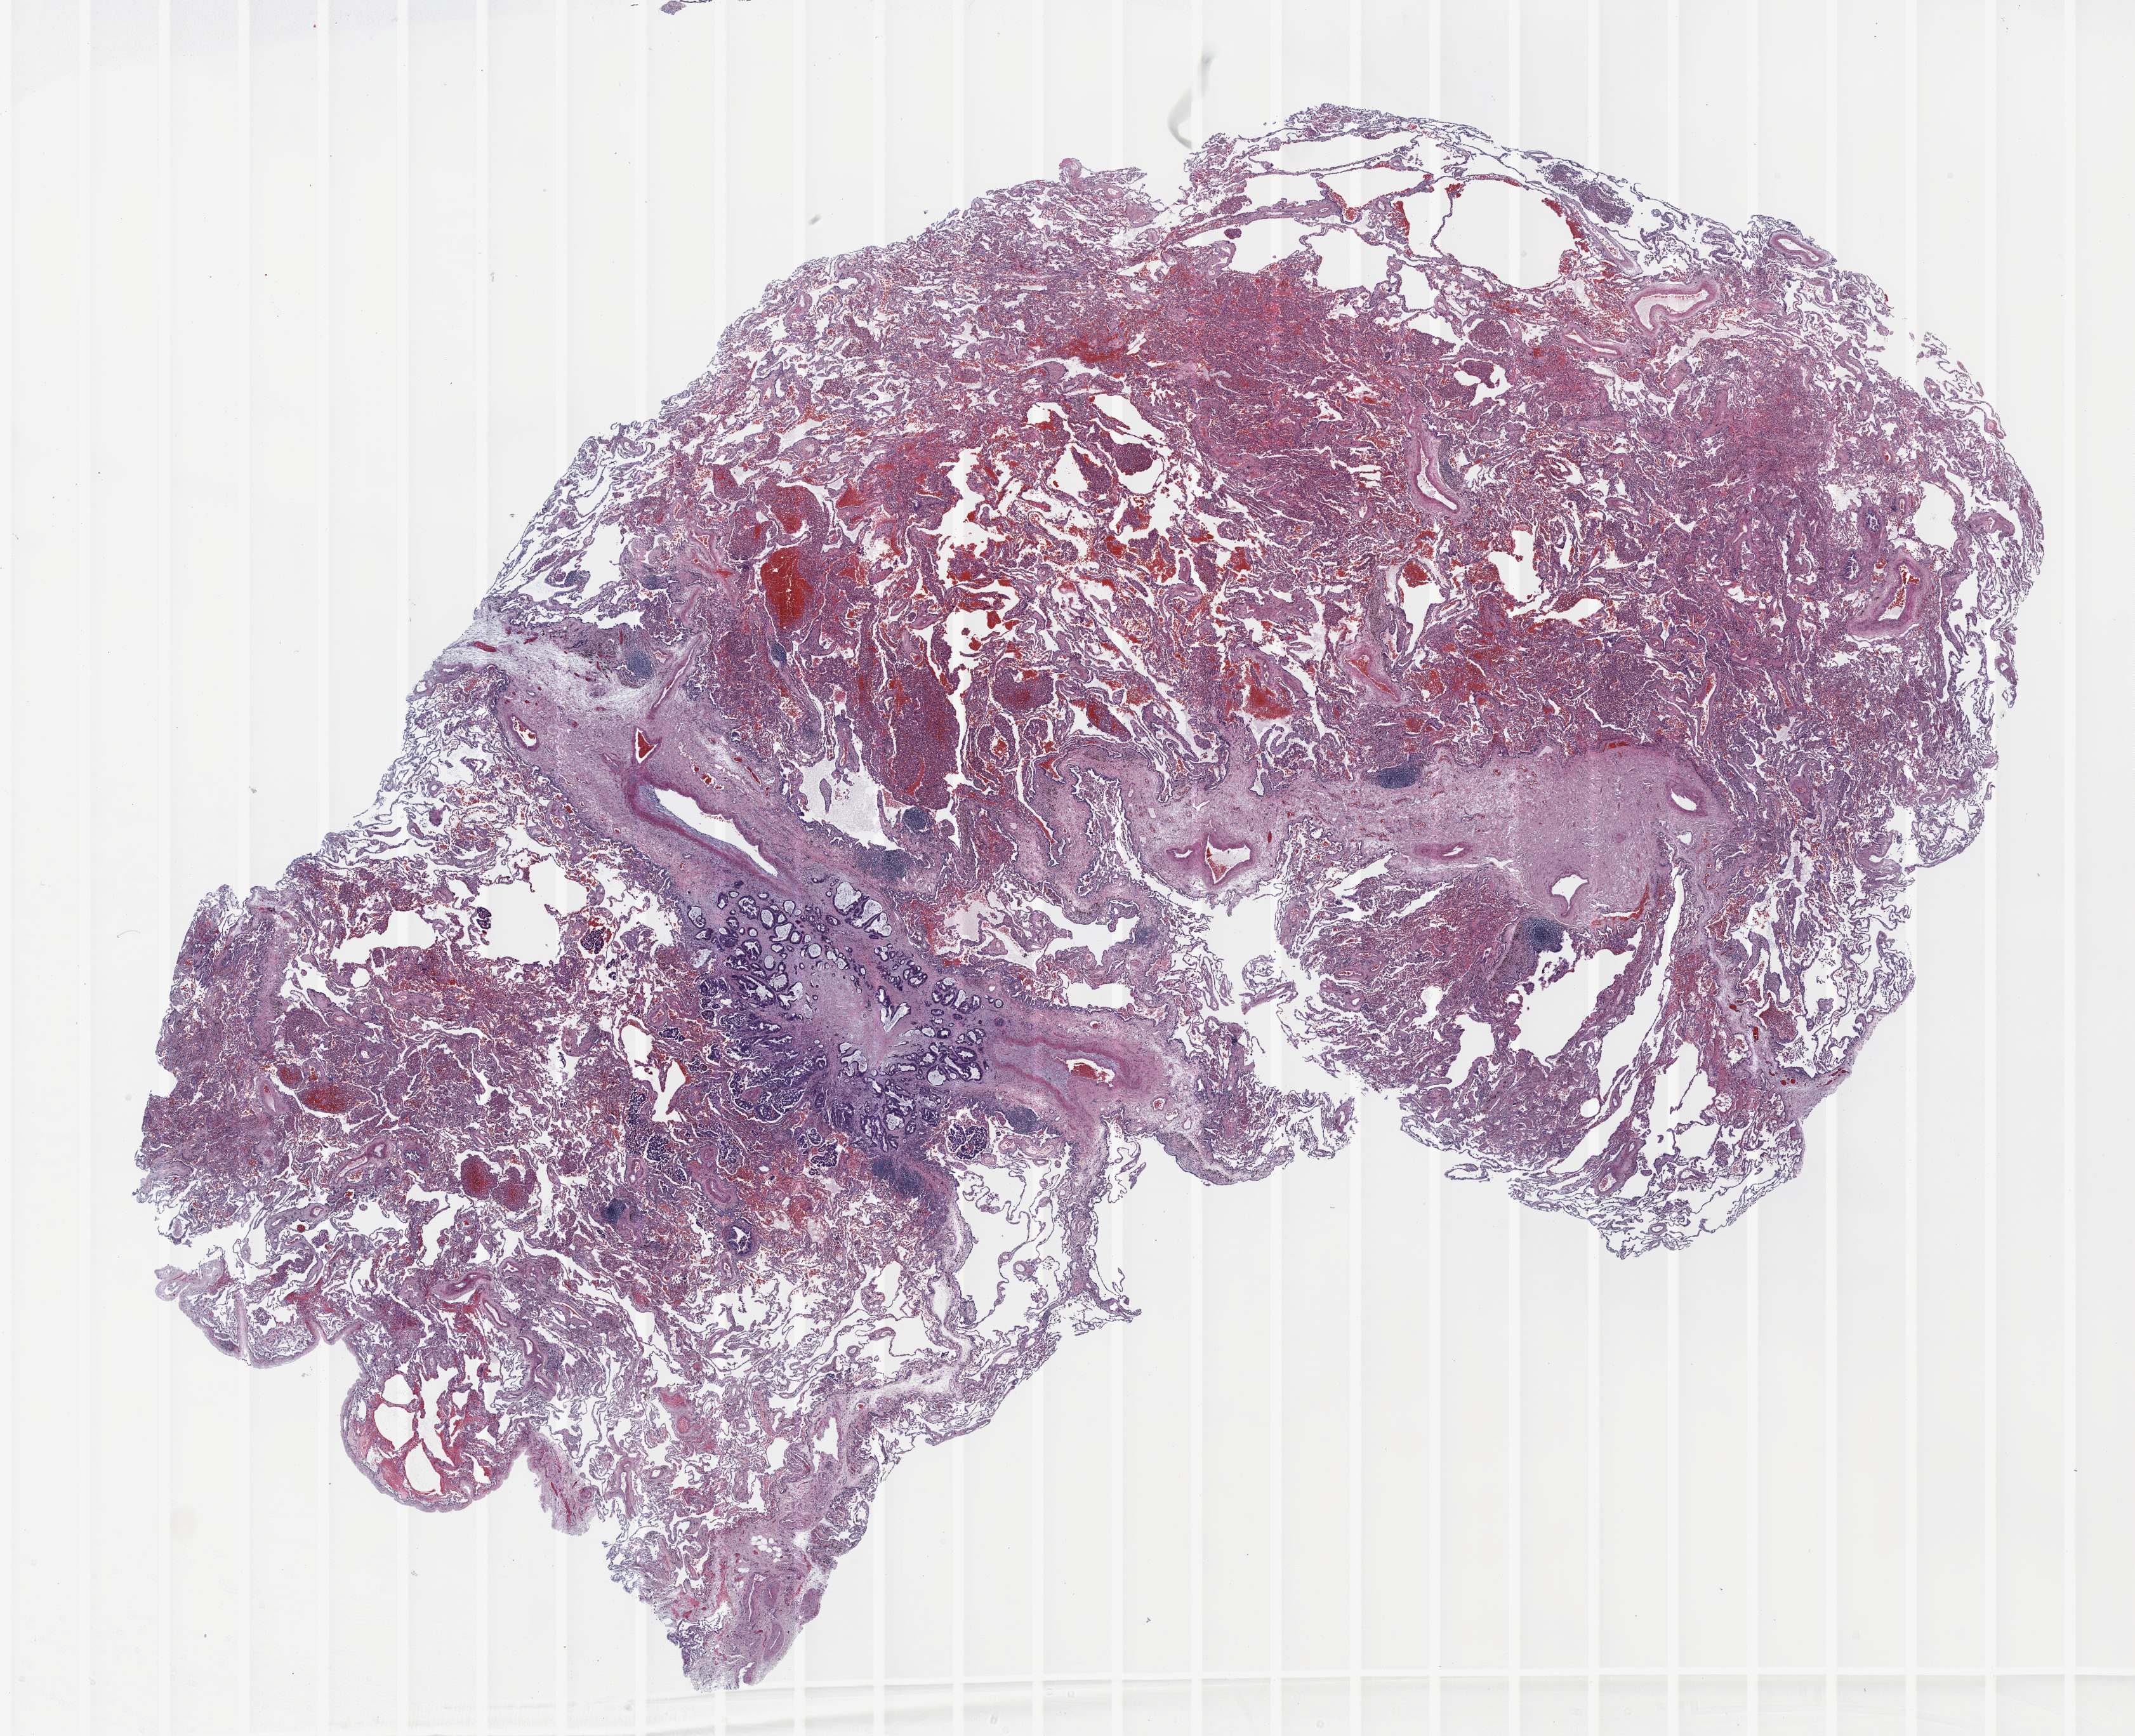
H&E-stained whole-slide image, a low-resolution overview of the entire scanned area, about 27.0 x 22.0 mm (acquisition: 20x scan); FFPE section; lung tissue. Male, age 58 at enrolment. Current smoker at enrolment. Grade: moderately differentiated (G2).
ICD-O-3 topography: middle lobe of lung (C34.2). Participant's lung-cancer diagnosis: Adenocarcinoma, NOS (ICD-O-3 8140/3). Stage (AJCC 6th edition): IIA. Tumour size (pathology): 10 mm. Primary tumour location (clinical record): right middle lobe.